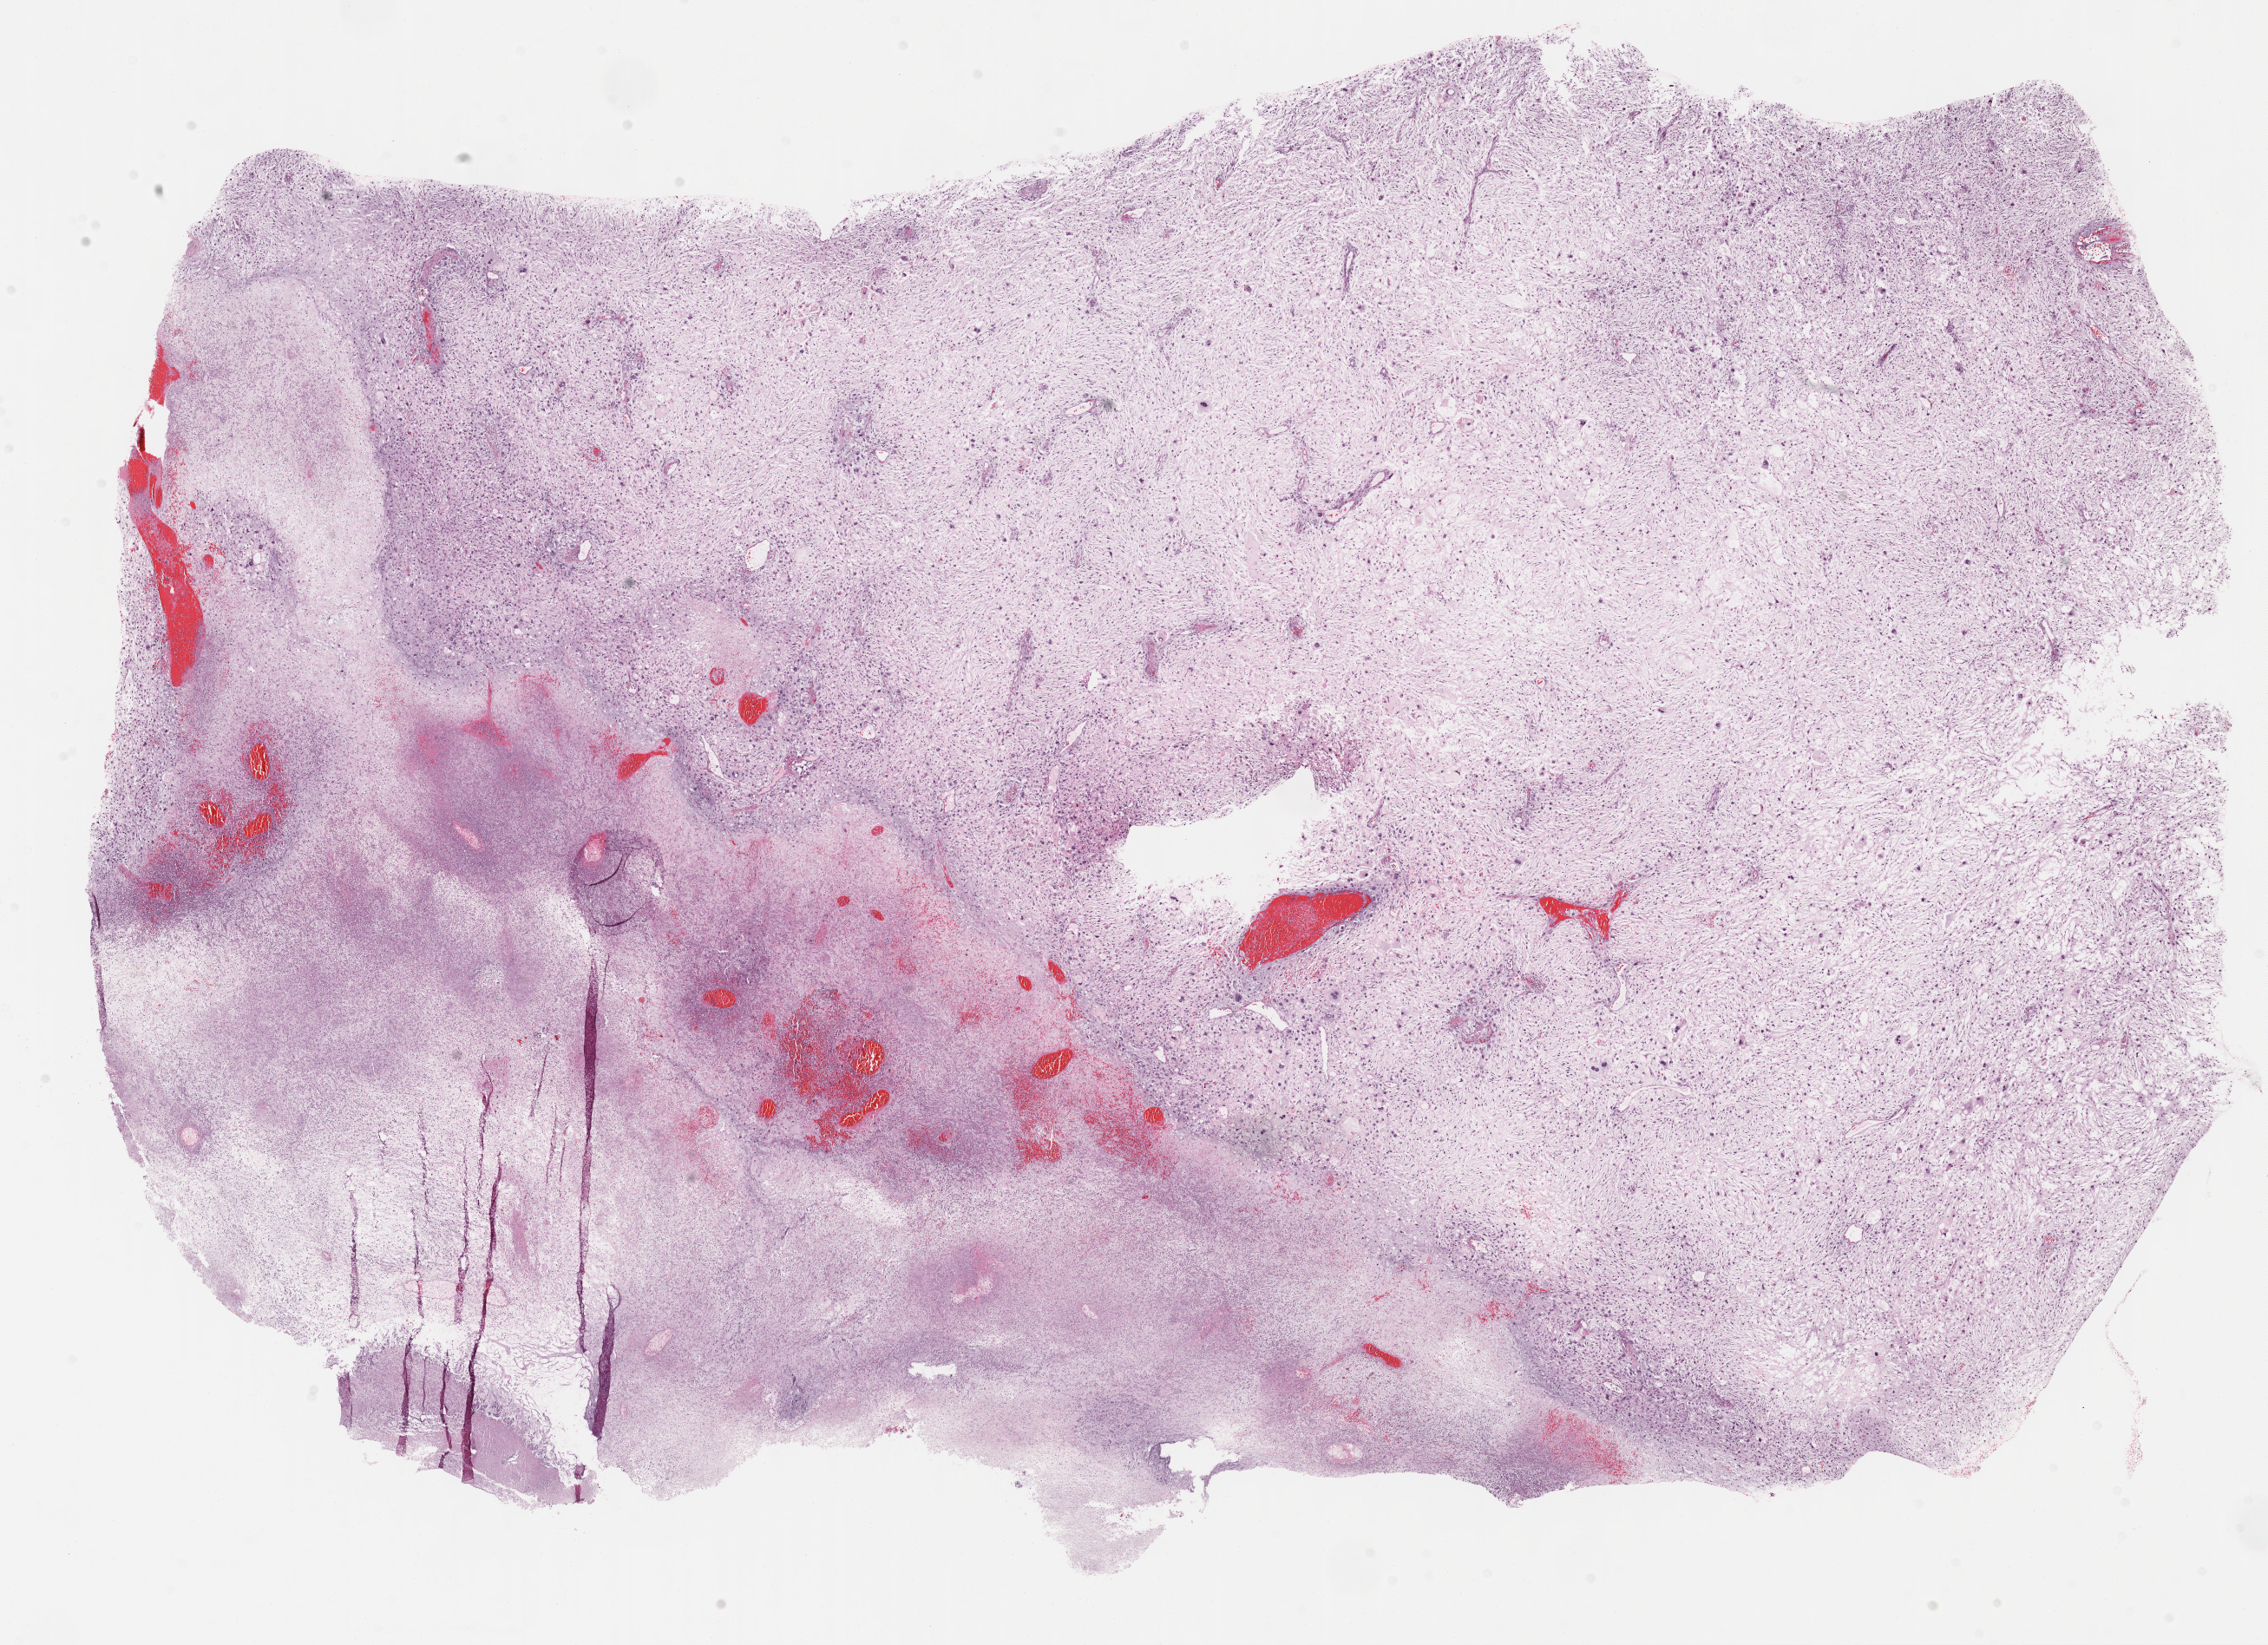
Whole-slide histology image, H&E, whole scanned area (about 21.1 x 15.3 mm, acquisition: 40x scan) shown as a low-resolution overview, formalin-fixed paraffin-embedded (FFPE) diagnostic section, primary tumour sample from the connective, subcutaneous and other soft tissues. Patient: male, age at initial diagnosis 74 years.
• pathologic diagnosis: Fibromyxosarcoma (connective, subcutaneous and other soft tissues of lower limb and hip)